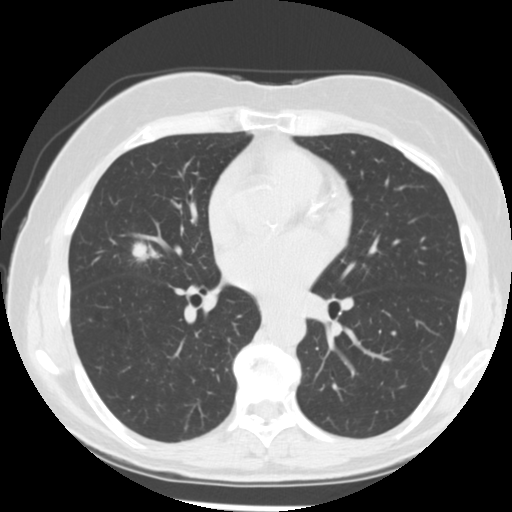
Low-dose screening chest CT, axial slice, baseline screening round, lung window (W 1500 / L -600 HU), 2.5 mm slice thickness, standard (soft-tissue) reconstruction kernel (STANDARD). Female participant, aged 66 years at enrolment. Former smoker at enrolment.
Lesion marked by an expert reader, box from (x=124, y=238) to (x=162, y=270) px. Screening reader's record for this exam (one nodule recorded; not confirmed to be the boxed lesion): non-calcified nodule or mass ≥4 mm, right middle lobe, 15 × 13 mm, poorly defined margins, soft tissue attenuation. Official screen result: positive, change unspecified: nodule(s) >= 4 mm or enlarging nodule(s), mass(es), or other non-specific abnormalities suspicious for lung cancer. Participant outcome: lung cancer diagnosed 27 days after this screen — adenocarcinoma, NOS, right middle lobe, undifferentiated (G4), stage IIIA (AJCC 6th edition), 18 mm at pathology.